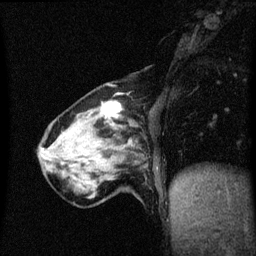
Breast MRI (dynamic contrast-enhanced), one sagittal slice. Dynamic contrast-enhanced series, image 2 of 3 at this slice position (ordered by acquisition). 1.5 T. TE 4.2 ms, TR 8.4 ms. 2 mm slice thickness. 256 × 256 image matrix. Female patient, age 64 years. From the clinical record (not read from this slice): setting: breast cancer imaged before/during neoadjuvant chemotherapy; receptor status: HR-positive, HER2-negative.
Structures marked on this image (semi-automatically segmented with operator editing):
- analysis volume of interest (the breast-tissue region the enhancement analysis was run in; not a lesion): bounding box <56,102,138,175> (left, top, right, bottom; pixels)
- tumour enhancement mask (voxels above the 70 % enhancement threshold inside the analysis volume of interest): <103,102,122,117>